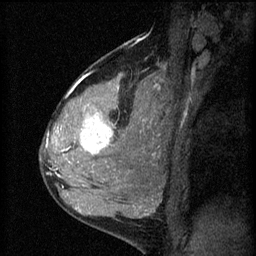
Breast MRI (dynamic contrast-enhanced), one sagittal slice; slice 40 of 60 in the series (ordered by position); 3 images stored at this slice position (order not interpretable as contrast timing); 1.5 T; TE 4.2 ms, TR 8.2 ms; 256 × 256 image matrix, field of view 180 × 180 mm. Patient: female, 37 years.
Outlined on this slice (semi-automatically segmented with operator editing):
- analysis volume of interest (the breast-tissue region the enhancement analysis was run in; not a lesion): bounding box (x1, y1, x2, y2) in pixels: (53, 78, 140, 181)
- tumour enhancement mask (voxels above the 70 % enhancement threshold inside the analysis volume of interest): (57, 112, 113, 155)